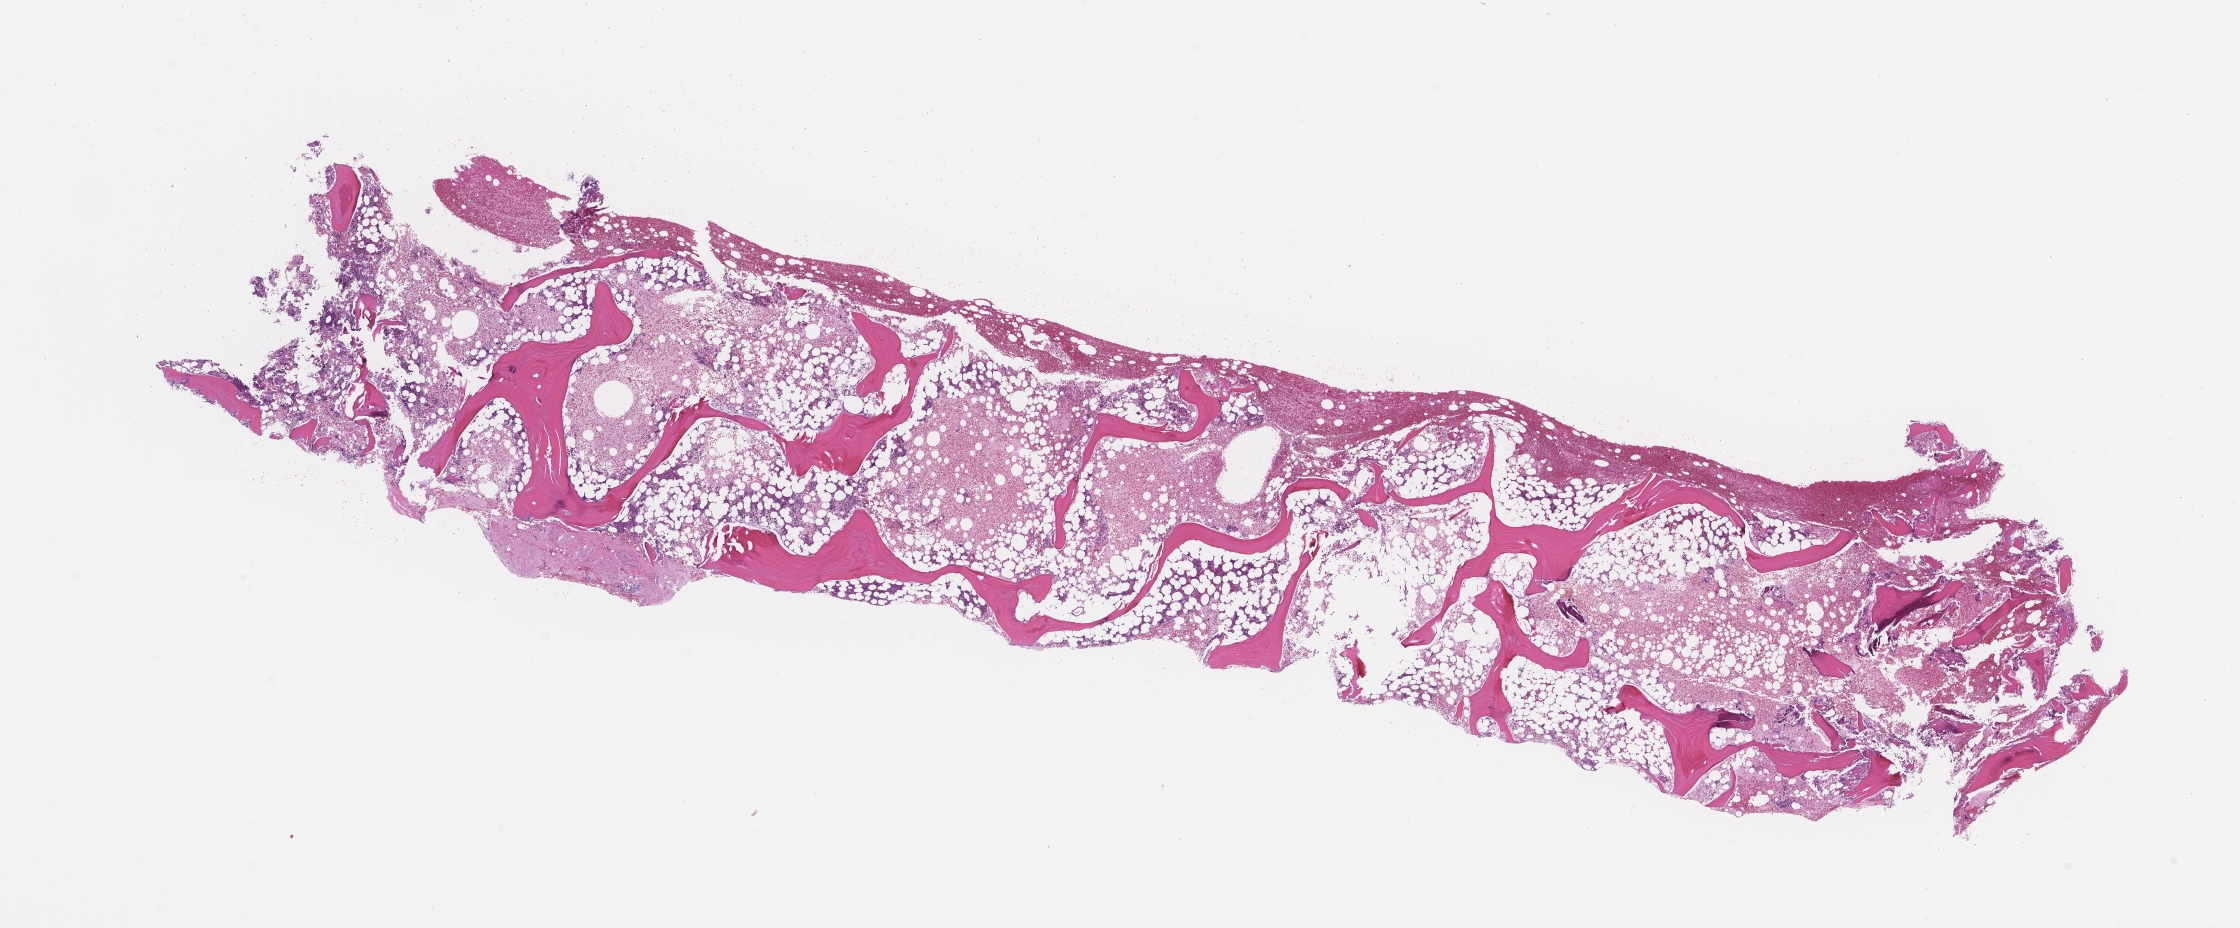
Hematoxylin and eosin (H&E) whole-slide image, a low-resolution overview of the entire scanned area, about 18.1 x 7.5 mm. FFPE section. Site: bone marrow. Specimen time point: archival tissue. Male patient.
This section: primary tumor. Diagnosis: Plasma Cell Myeloma.